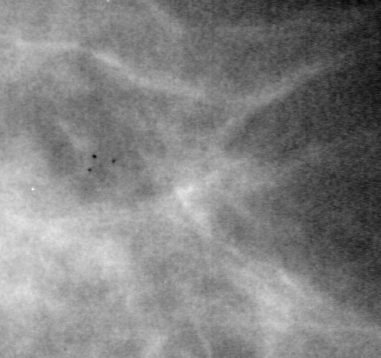
Region of interest cut from a scanned film mammogram (one marked finding), right breast, CC view.
Marked abnormality: mass, shape irregular, margins ill defined; BI-RADS assessment category 4; subtlety rating 4 on a 1 (subtle) to 5 (obvious) scale; pathology (as recorded): malignant.